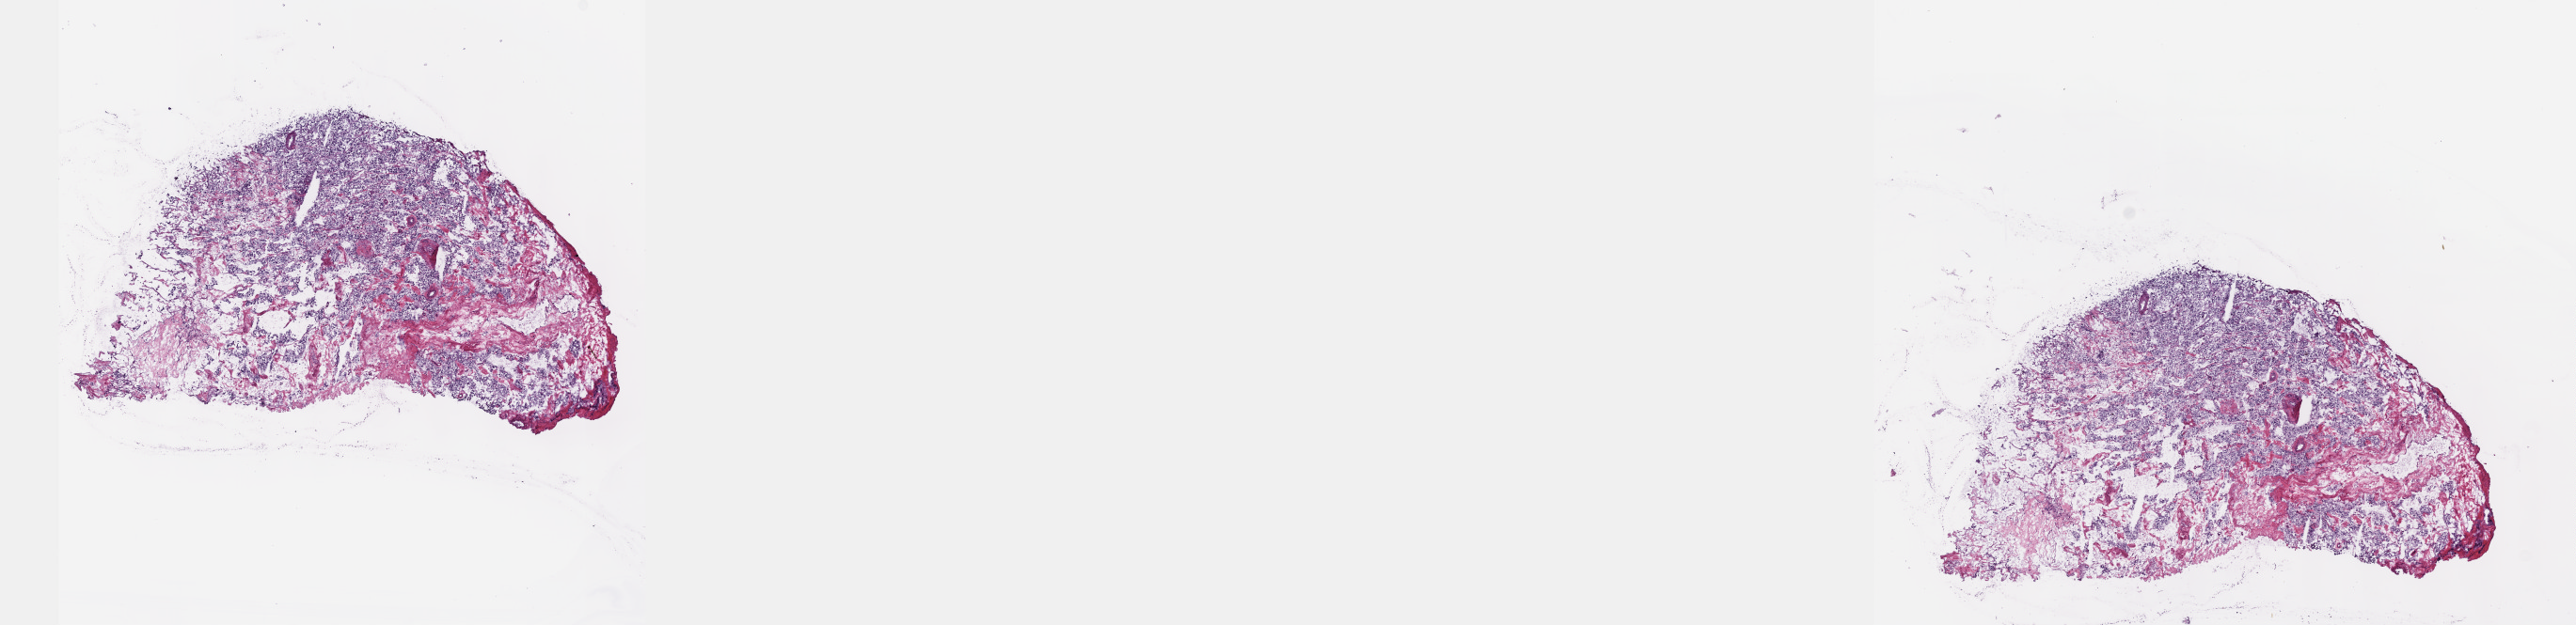
Whole-slide histology image, Hematoxylin and eosin (H&E) stained, a low-resolution overview of the entire scanned area, about 22.1 x 5.4 mm; frozen section from the top of the tissue portion; sample: primary tumour, adrenal gland. Female, age 83 years at initial diagnosis. Composition of this section per pathologist review: tumour cells 95%, tumour nuclei 95%, normal cells 0%, stromal cells 5%, necrosis 0%. Infiltration values recorded for this section: lymphocyte infiltration 0%, monocyte infiltration 0%, neutrophil infiltration 0%.
Laterality: left. Pathologic diagnosis: Pheochromocytoma, NOS.